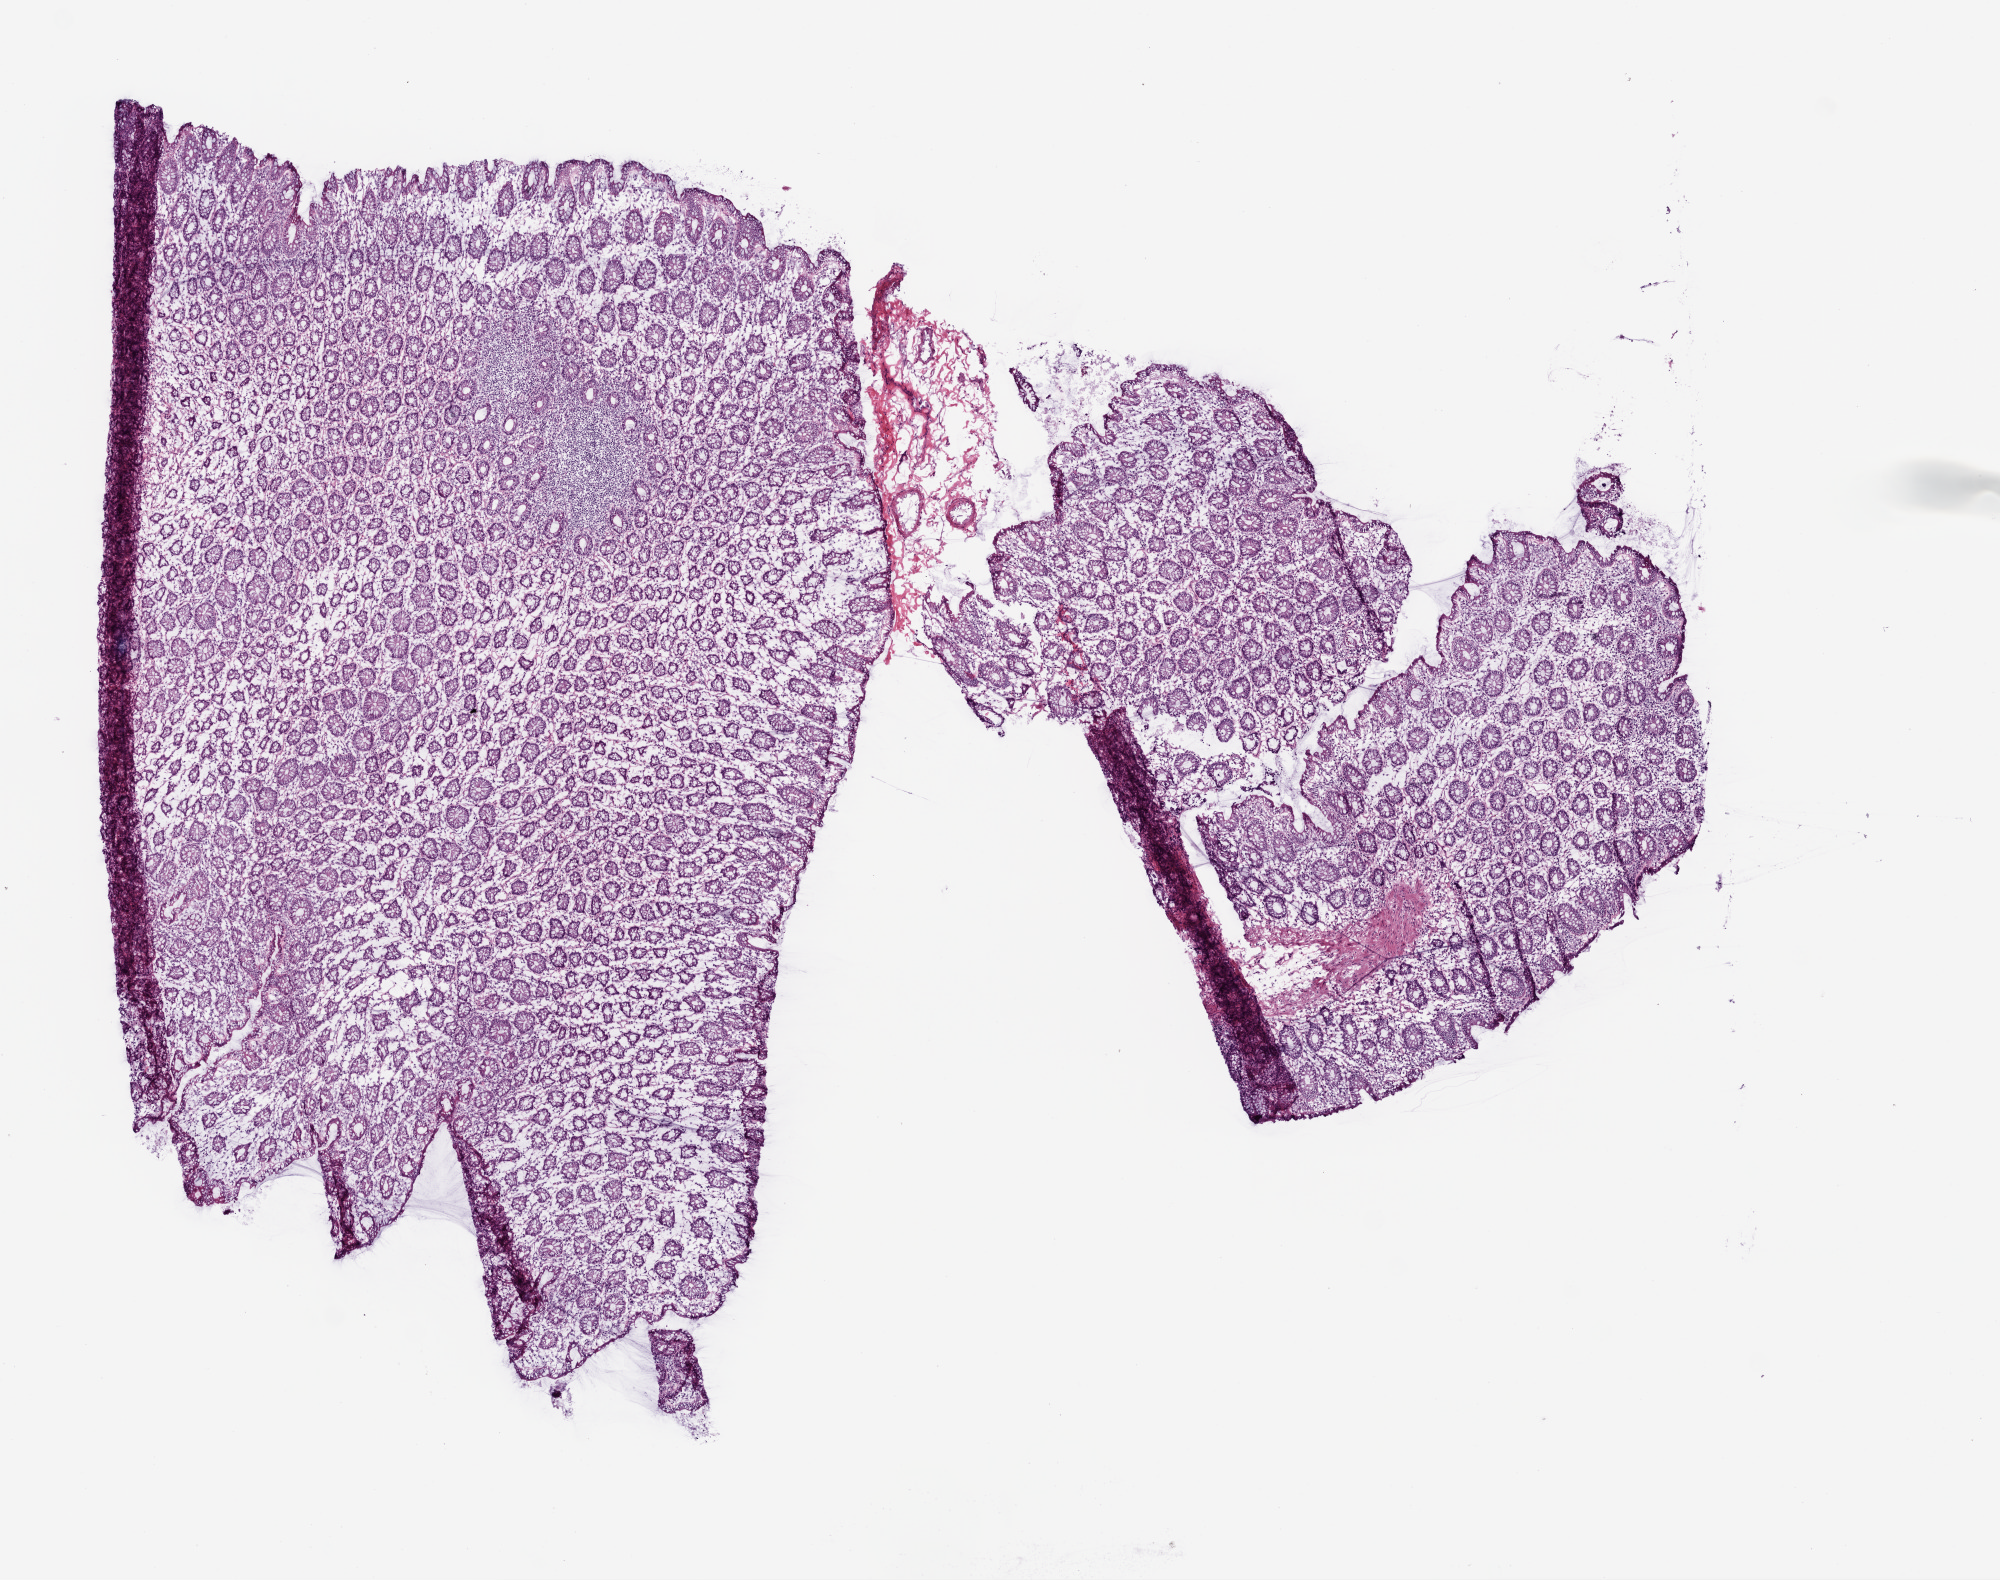
H&E whole-slide image — low-resolution overview of the scanned area, about 8.0 x 6.3 mm. Frozen section from the top of the tissue portion. Colon, solid tissue normal (non-tumour tissue) sample. Male patient; age at initial diagnosis 70 years.
This section: solid tissue normal (non-tumour) sample from the same patient. Patient diagnosis: Adenocarcinoma, NOS (ascending colon).